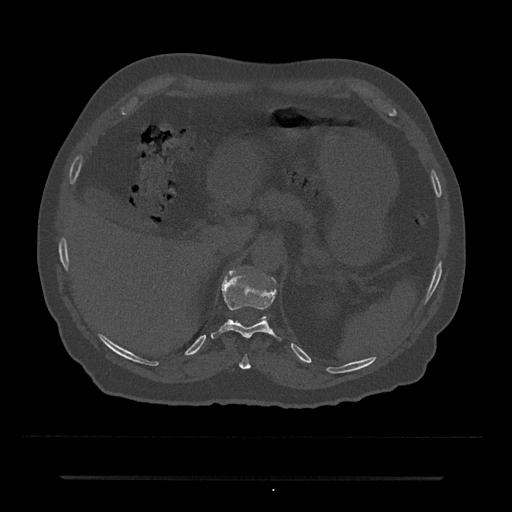
CT including the spine, one axial slice. Position 178 of 797 along the scan axis. Reconstruction kernel Br40s/3. 120 kVp. Bone window (W 1800 / L 400 HU). 0.5 mm slice thickness. 512 × 512 image matrix. Male patient, age 69 years. From the clinical record (not read from this slice): primary cancer: prostate.
Structures marked on this image (semi-automatic segmentation, software-assisted and operator-edited):
- T10 vertebra: box from (x=239, y=355) to (x=251, y=369) px
- T11 vertebra: (x=211, y=273)–(x=282, y=341)
- T12 vertebra: (x=263, y=279)–(x=275, y=319)